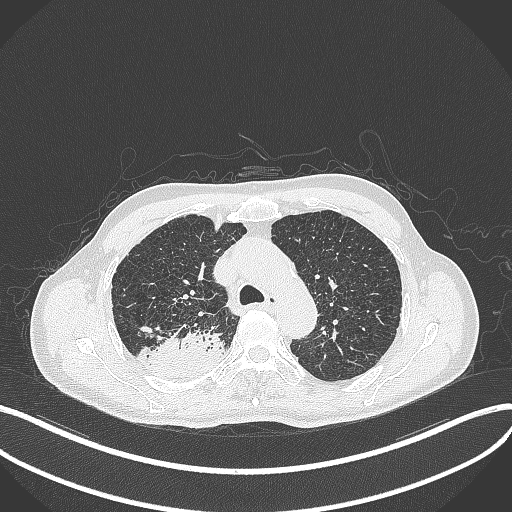
Chest CT, one axial slice. Slice 327 of 428 in the series (ordered by position). Reconstruction kernel B70f. 120 kVp. Lung window (W 1500 / L -600 HU). 1 mm slice thickness. 512 × 512 image matrix, field of view 400 × 400 mm. Male patient, age 79 years. Case-level facts recorded for this patient, not image findings: clinical TNM (as recorded): T3 N0 M0.
Annotated regions visible in this slice (bounding box drawn by a radiologist):
- lung tumour (recorded histology: adenocarcinoma): bounding box <147,325,226,380> (left, top, right, bottom; pixels)